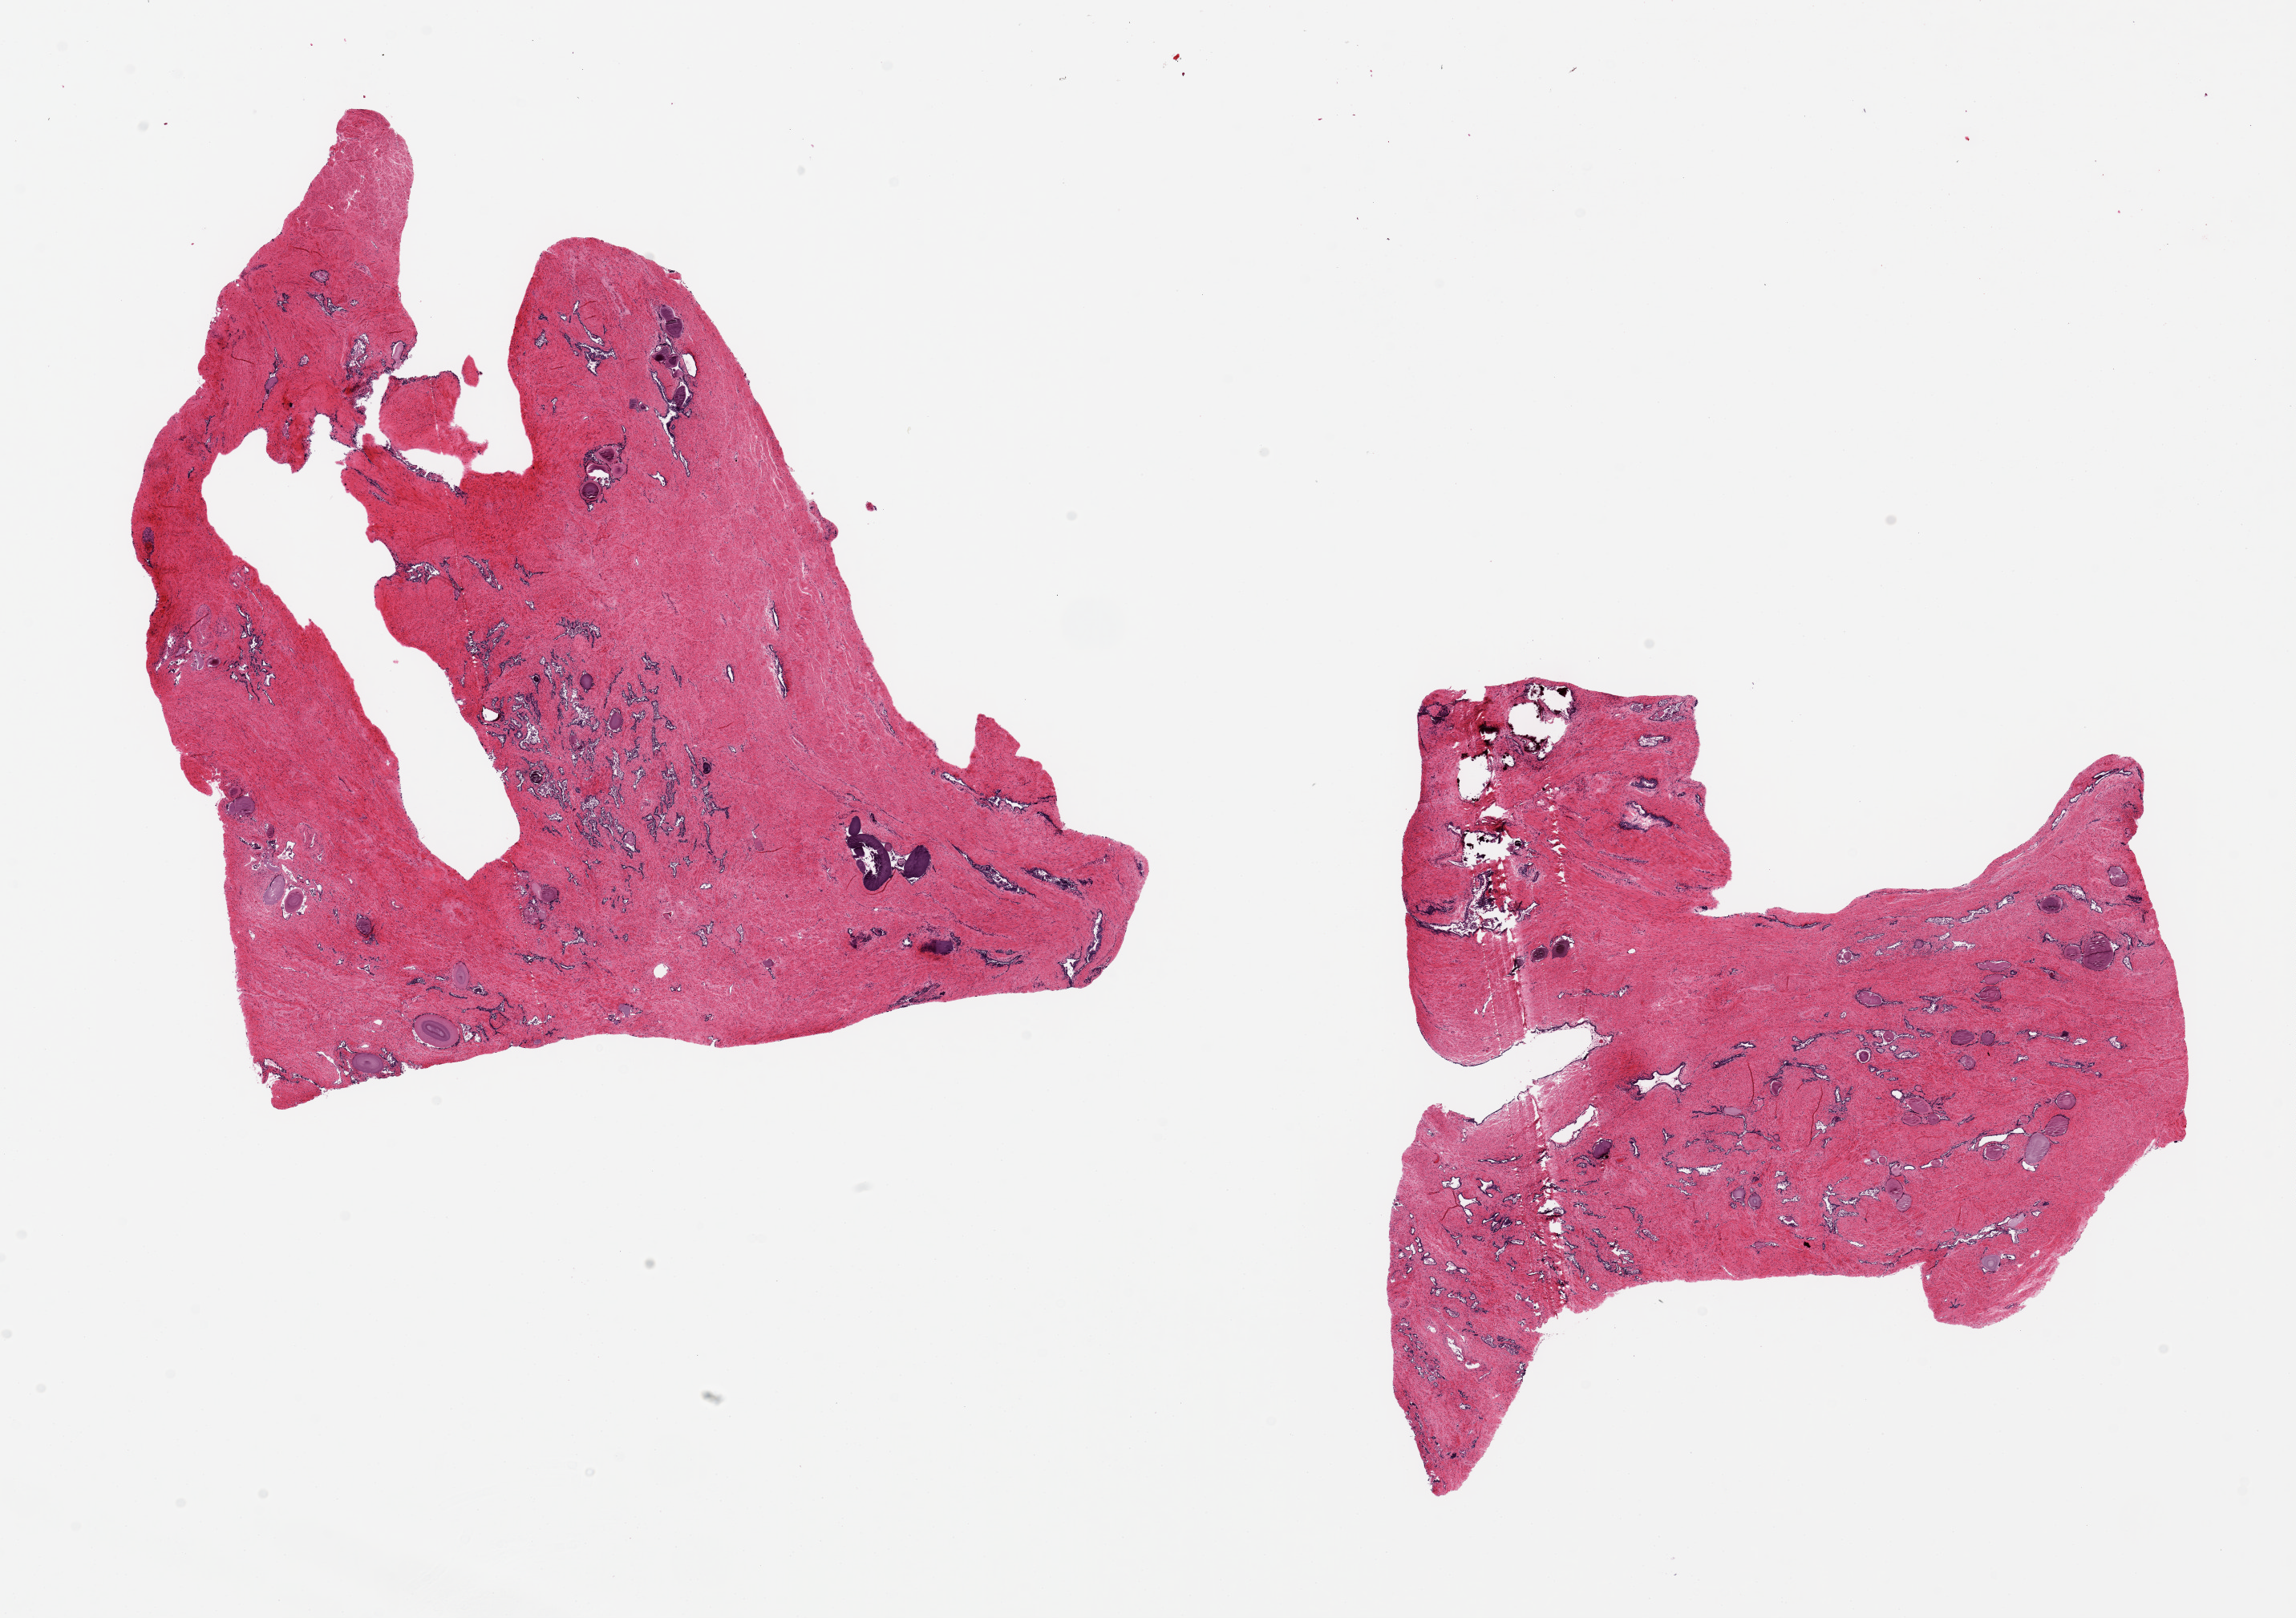
Hematoxylin and eosin (H&E) whole-slide image, brightfield, a low-resolution overview of the entire scanned area, about 22.6 x 16.0 mm; PAXgene-fixed paraffin-embedded (PFPE) section; section of prostate (target tissue); donor tissue sample. Donor: male.
Reviewer comment on this tissue sample: 2 pieces, 10x9 & 8x8mm; mostly fibromuscular.